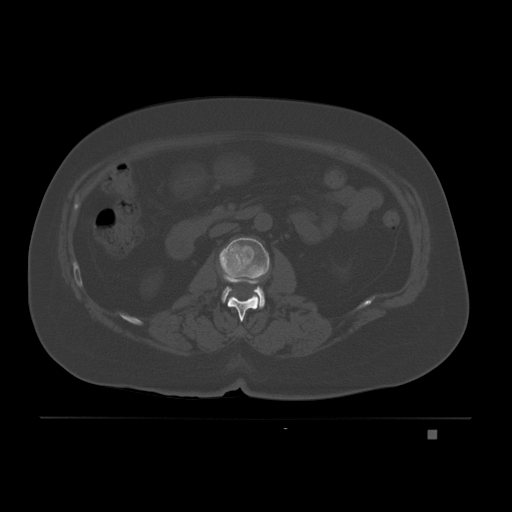
CT including the spine, one axial slice. Slice 67 of 221 in the series (ordered by position). Bone window (W 1800 / L 400 HU). 3 mm slice thickness. 512 × 512 image matrix, field of view 474 × 474 mm. Patient: female, 63 years. Case-level facts recorded for this patient, not image findings: primary cancer: breast.
Outlined on this slice (semi-automatic segmentation, software-assisted and operator-edited):
- L1 vertebra: bounding box [x1, y1, x2, y2] px = [222, 270, 265, 322]
- L2 vertebra: [219, 237, 270, 308]